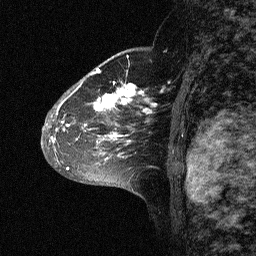
Breast MRI (dynamic contrast-enhanced), one sagittal slice. Slice 42 of 64 in the series (ordered by position). Dynamic contrast-enhanced study with each time point stored as its own series, time point 2 of 3 at this slice position (early post-contrast, ordered by acquisition time). 1.5 T. TE 4.5 ms, TR 11 ms. 256 × 256 image matrix, field of view 200 × 200 mm. Female patient, age 46 years. From the clinical record (not read from this slice): setting: breast cancer imaged before/during neoadjuvant chemotherapy; receptor status: HER2-positive.
Outlined on this slice (semi-automatic segmentation, software-assisted and operator-edited):
- analysis volume of interest (the breast-tissue region the enhancement analysis was run in; not a lesion): bounding box [x1, y1, x2, y2] px = [43, 72, 164, 177]
- tumour enhancement mask (voxels above the 90 % enhancement threshold inside the analysis volume of interest): [50, 72, 163, 170]